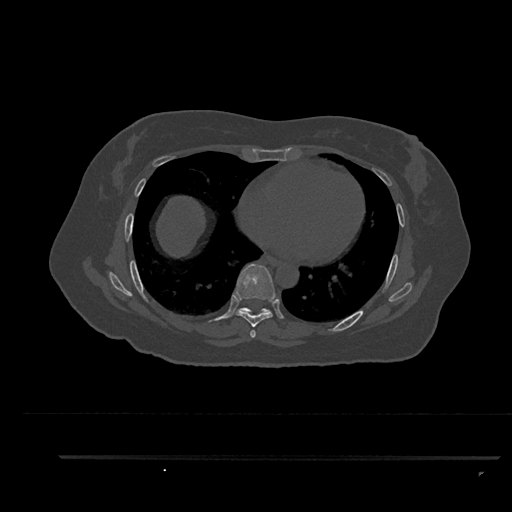
CT including the spine, one axial slice; position 497 of 797 along the scan axis; reconstruction kernel Br40s/3; 120 kVp; bone window (W 1800 / L 400 HU); 0.5 mm slice thickness; 512 × 512 image matrix, field of view 408 × 408 mm. Patient: female, 44 years. Case-level facts recorded for this patient, not image findings: primary cancer: renal; vertebrae with lytic lesions (as recorded): L1.
Annotated regions visible in this slice (semi-automatic segmentation, software-assisted and operator-edited):
- T6 vertebra: bounding box (x1, y1, x2, y2) in pixels: (252, 333, 255, 337)
- T7 vertebra: (233, 264, 276, 338)
- T8 vertebra: (236, 308, 270, 315)